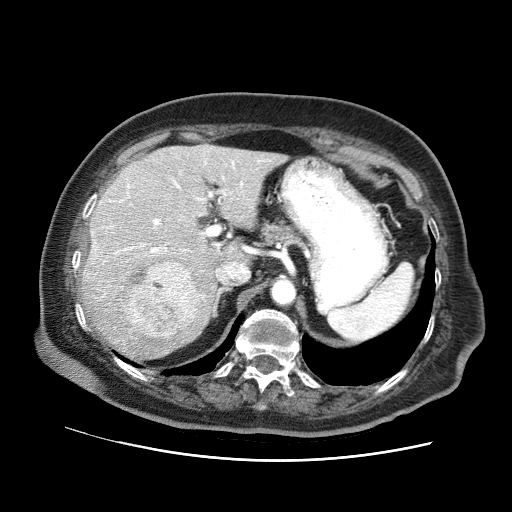
Contrast-enhanced abdominal CT (liver protocol), one axial slice. Slice 44 of 73 in the series (ordered by position). Reconstruction kernel STANDARD. Soft-tissue window (W 400 / L 40 HU). 2.5 mm slice thickness. 512 × 512 image matrix. Case-level facts recorded for this patient, not image findings: diagnosis: hepatocellular carcinoma (patient treated with transarterial chemoembolisation; whether this scan precedes or follows treatment is not stated here); TNM stage (as recorded): Stage-I; Child-Pugh class: A; tumour differentiation: well differentiated; tumour nodularity: uninodular.
Annotated regions visible in this slice (semi-automatically segmented with operator editing):
- liver parenchyma outside the tumour (the mass and vessels are separate outlines, so this box may not span the whole liver): bounding box (x1, y1, x2, y2) in pixels: (82, 144, 286, 363)
- mass: (122, 261, 201, 338)
- liver vessels: (92, 160, 261, 298)